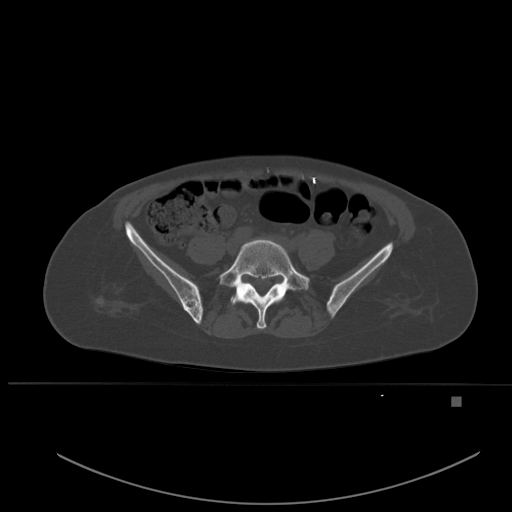
CT including the spine, one axial slice; slice 154 of 651 in the series (ordered by position); bone window (W 1800 / L 400 HU); 1.5 mm slice thickness; 512 × 512 image matrix. Female patient, age 49 years. Case-level facts recorded for this patient, not image findings: primary cancer: breast.
Structures marked on this image (semi-automatic segmentation, software-assisted and operator-edited):
- L5 vertebra: bounding box <219,239,310,329> (left, top, right, bottom; pixels)